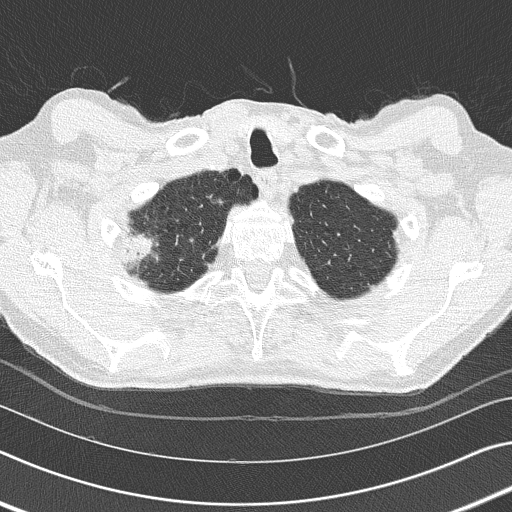
Low-dose screening chest CT, one axial slice; position 144 of 155 along the scan axis; 120 kVp; lung window (W 1500 / L -600 HU); 2 mm slice thickness; 512 × 512 image matrix.
Outlined on this slice (manually delineated by an expert):
- lesion 1 (tumor, middle lobe of right lung): bounding box <124,230,157,276> (left, top, right, bottom; pixels)